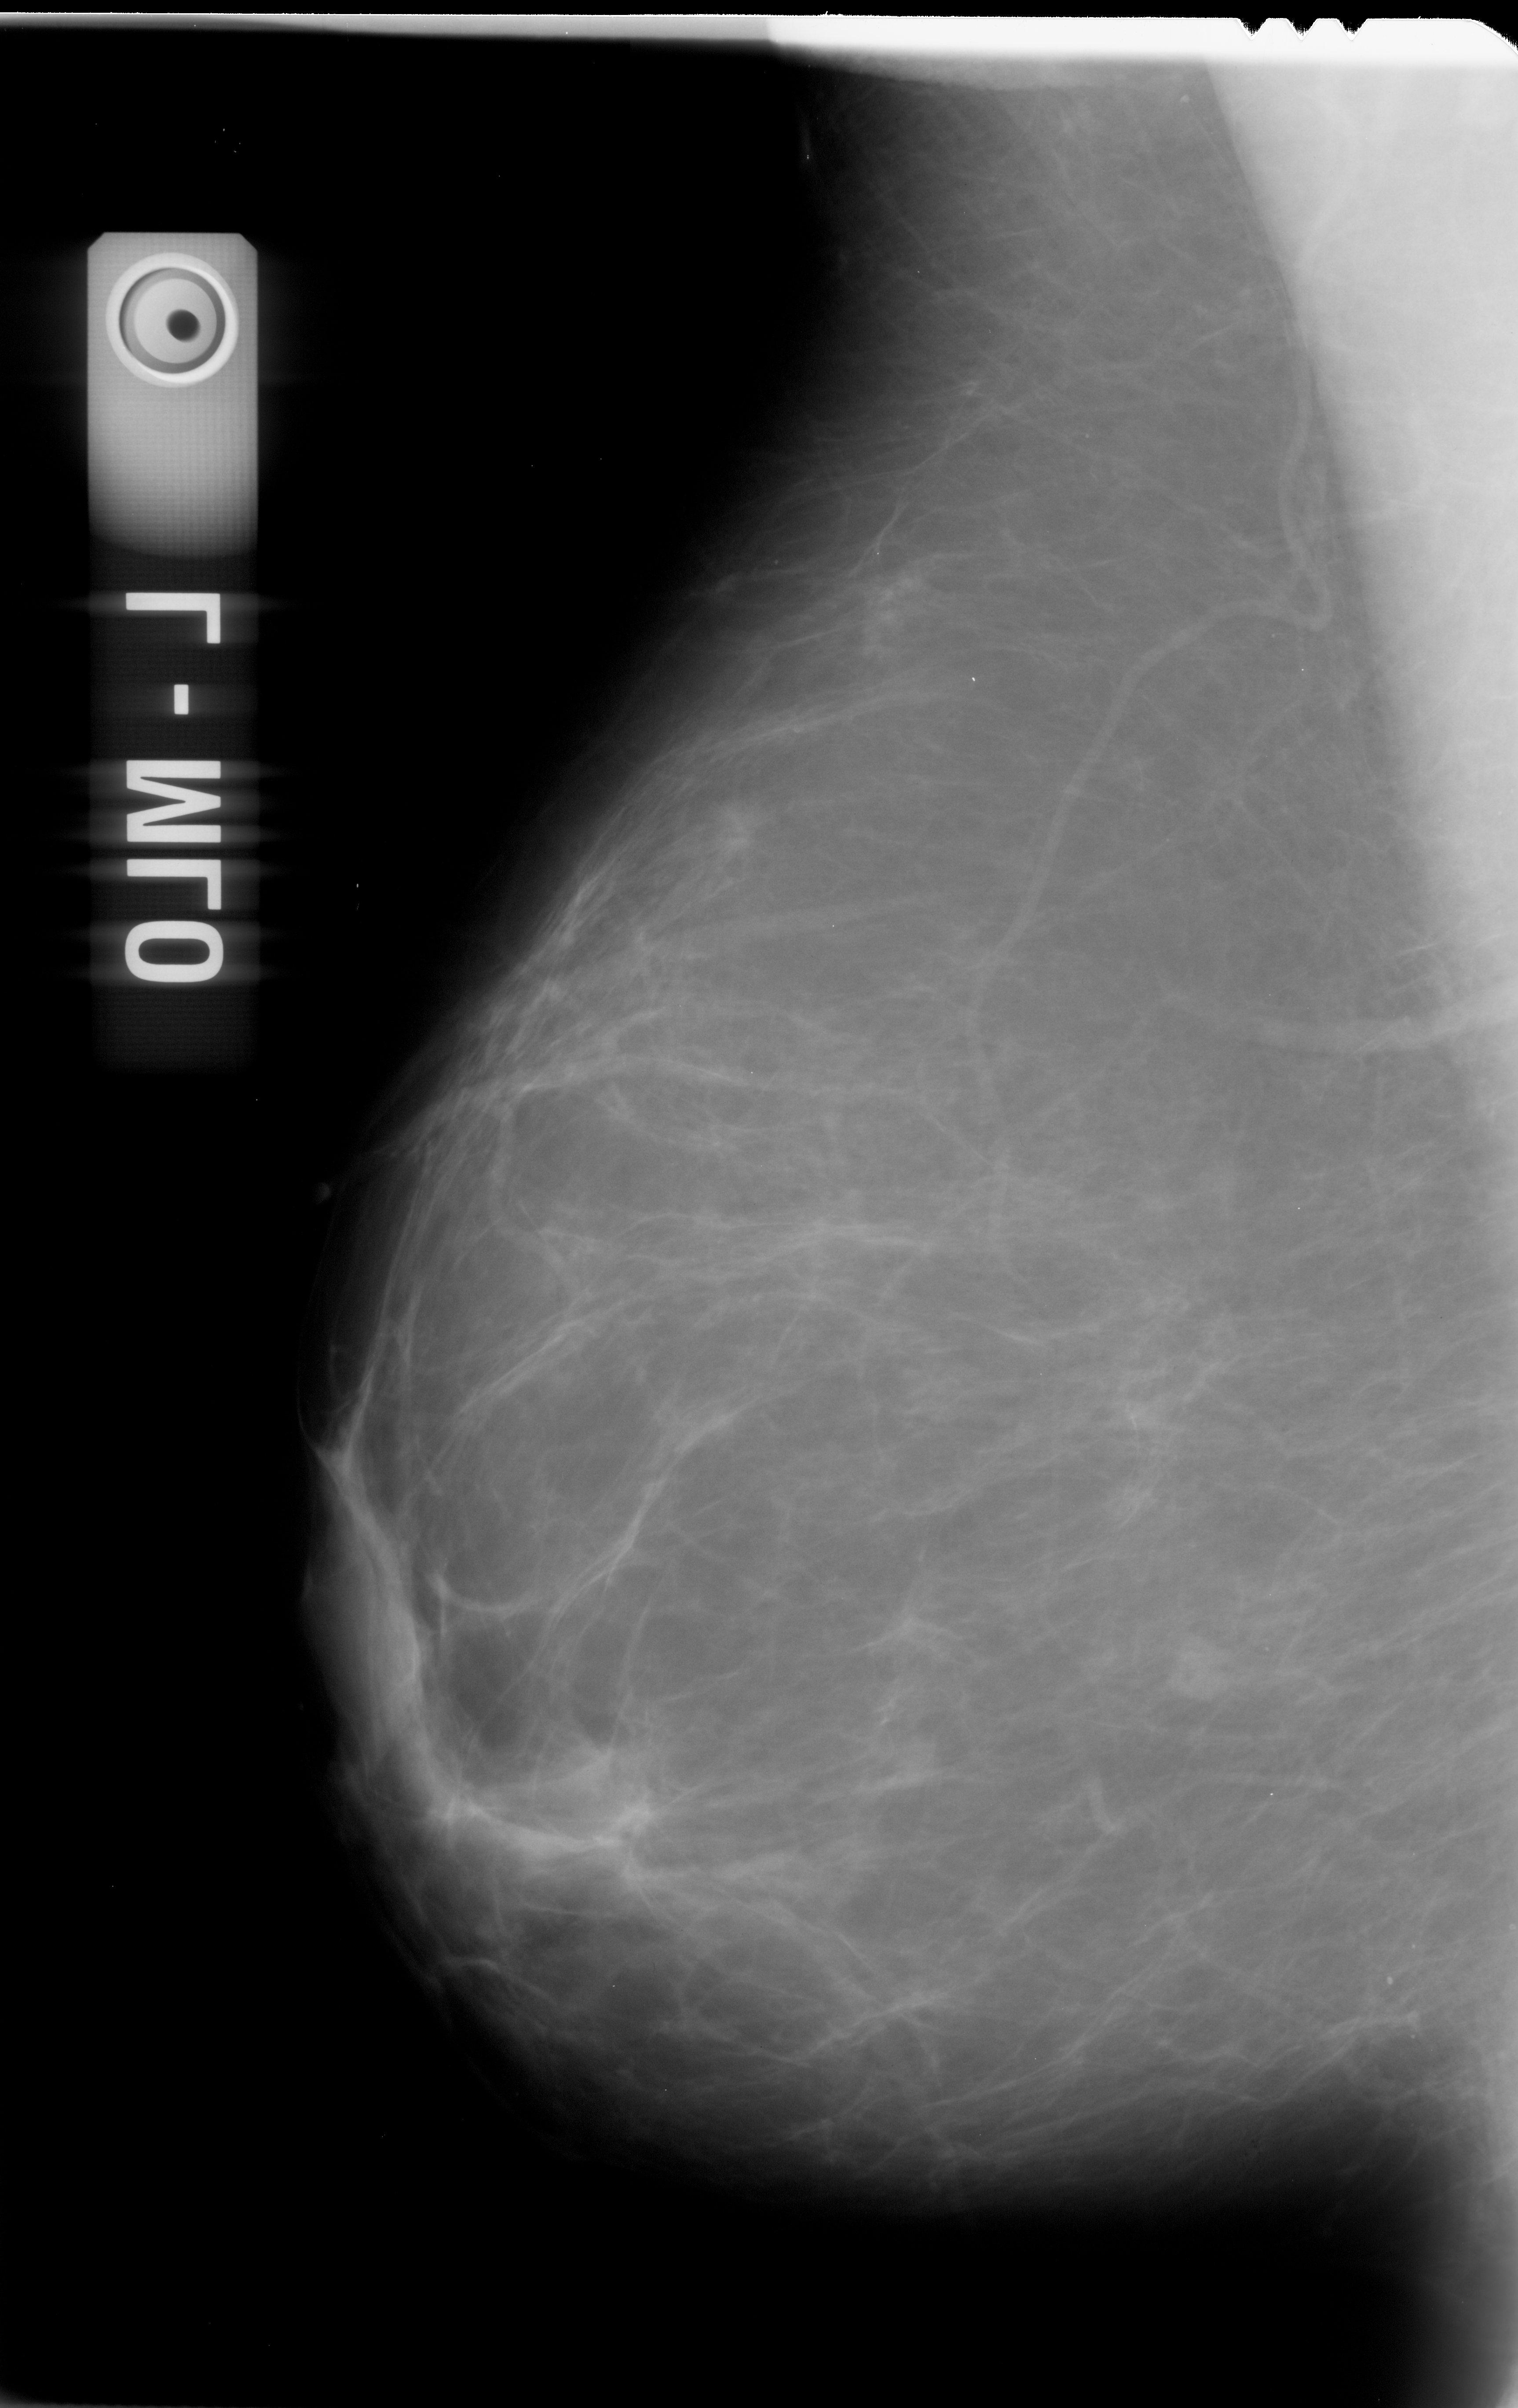
Scanned film-screen mammogram. Left breast. Mediolateral oblique (MLO) view. BI-RADS breast density category 2 (scale 1–4). 1518 × 2408 image matrix.
Marked abnormalities (boxes around the expert regions of interest):
- mass, shape irregular, margins spiculated; BI-RADS assessment category 4; pathology result (as recorded, not read from the image): malignant: box from (x=692, y=792) to (x=772, y=887) px